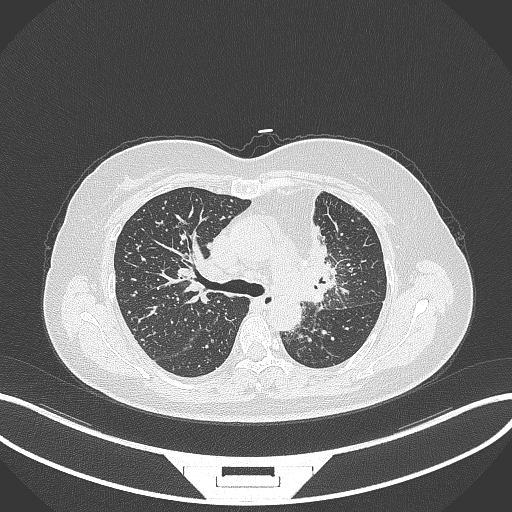
Chest CT, one axial slice. Position 218 of 348 along the scan axis. Reconstruction kernel B70f. 120 kVp. Lung window (W 1500 / L -600 HU). 1 mm slice thickness. 512 × 512 image matrix, field of view 400 × 400 mm. Female patient, age 49 years. From the clinical record (not read from this slice): clinical TNM (as recorded): T1c N0 M1.
Annotated regions visible in this slice (rectangle marked by the reading radiologist):
- lung tumour (recorded histology: adenocarcinoma): bounding box [x1, y1, x2, y2] px = [292, 190, 335, 311]